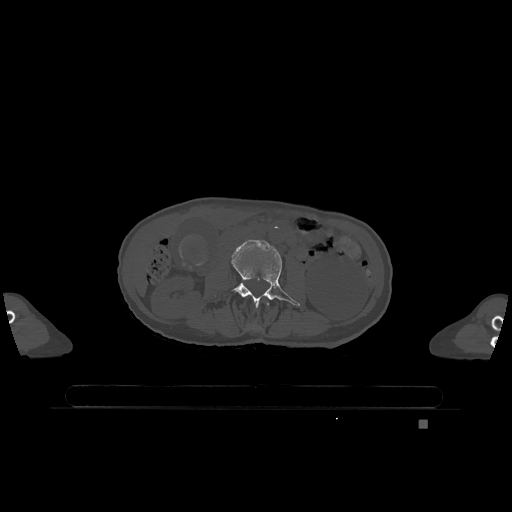
CT including the spine, one axial slice. Slice 359 of 1317 in the series (ordered by position). Bone window (W 1800 / L 400 HU). 0.5 mm slice thickness. 512 × 512 image matrix. Patient: female, 74 years. Case-level facts recorded for this patient, not image findings: primary cancer: lung; vertebrae with lytic lesions (as recorded): T1, T4, T5, T6, L4, L5.
Structures marked on this image (semi-automatic segmentation, software-assisted and operator-edited):
- L2 vertebra: bounding box (x1, y1, x2, y2) in pixels: (266, 303, 269, 305)
- L3 vertebra: (215, 240, 300, 308)